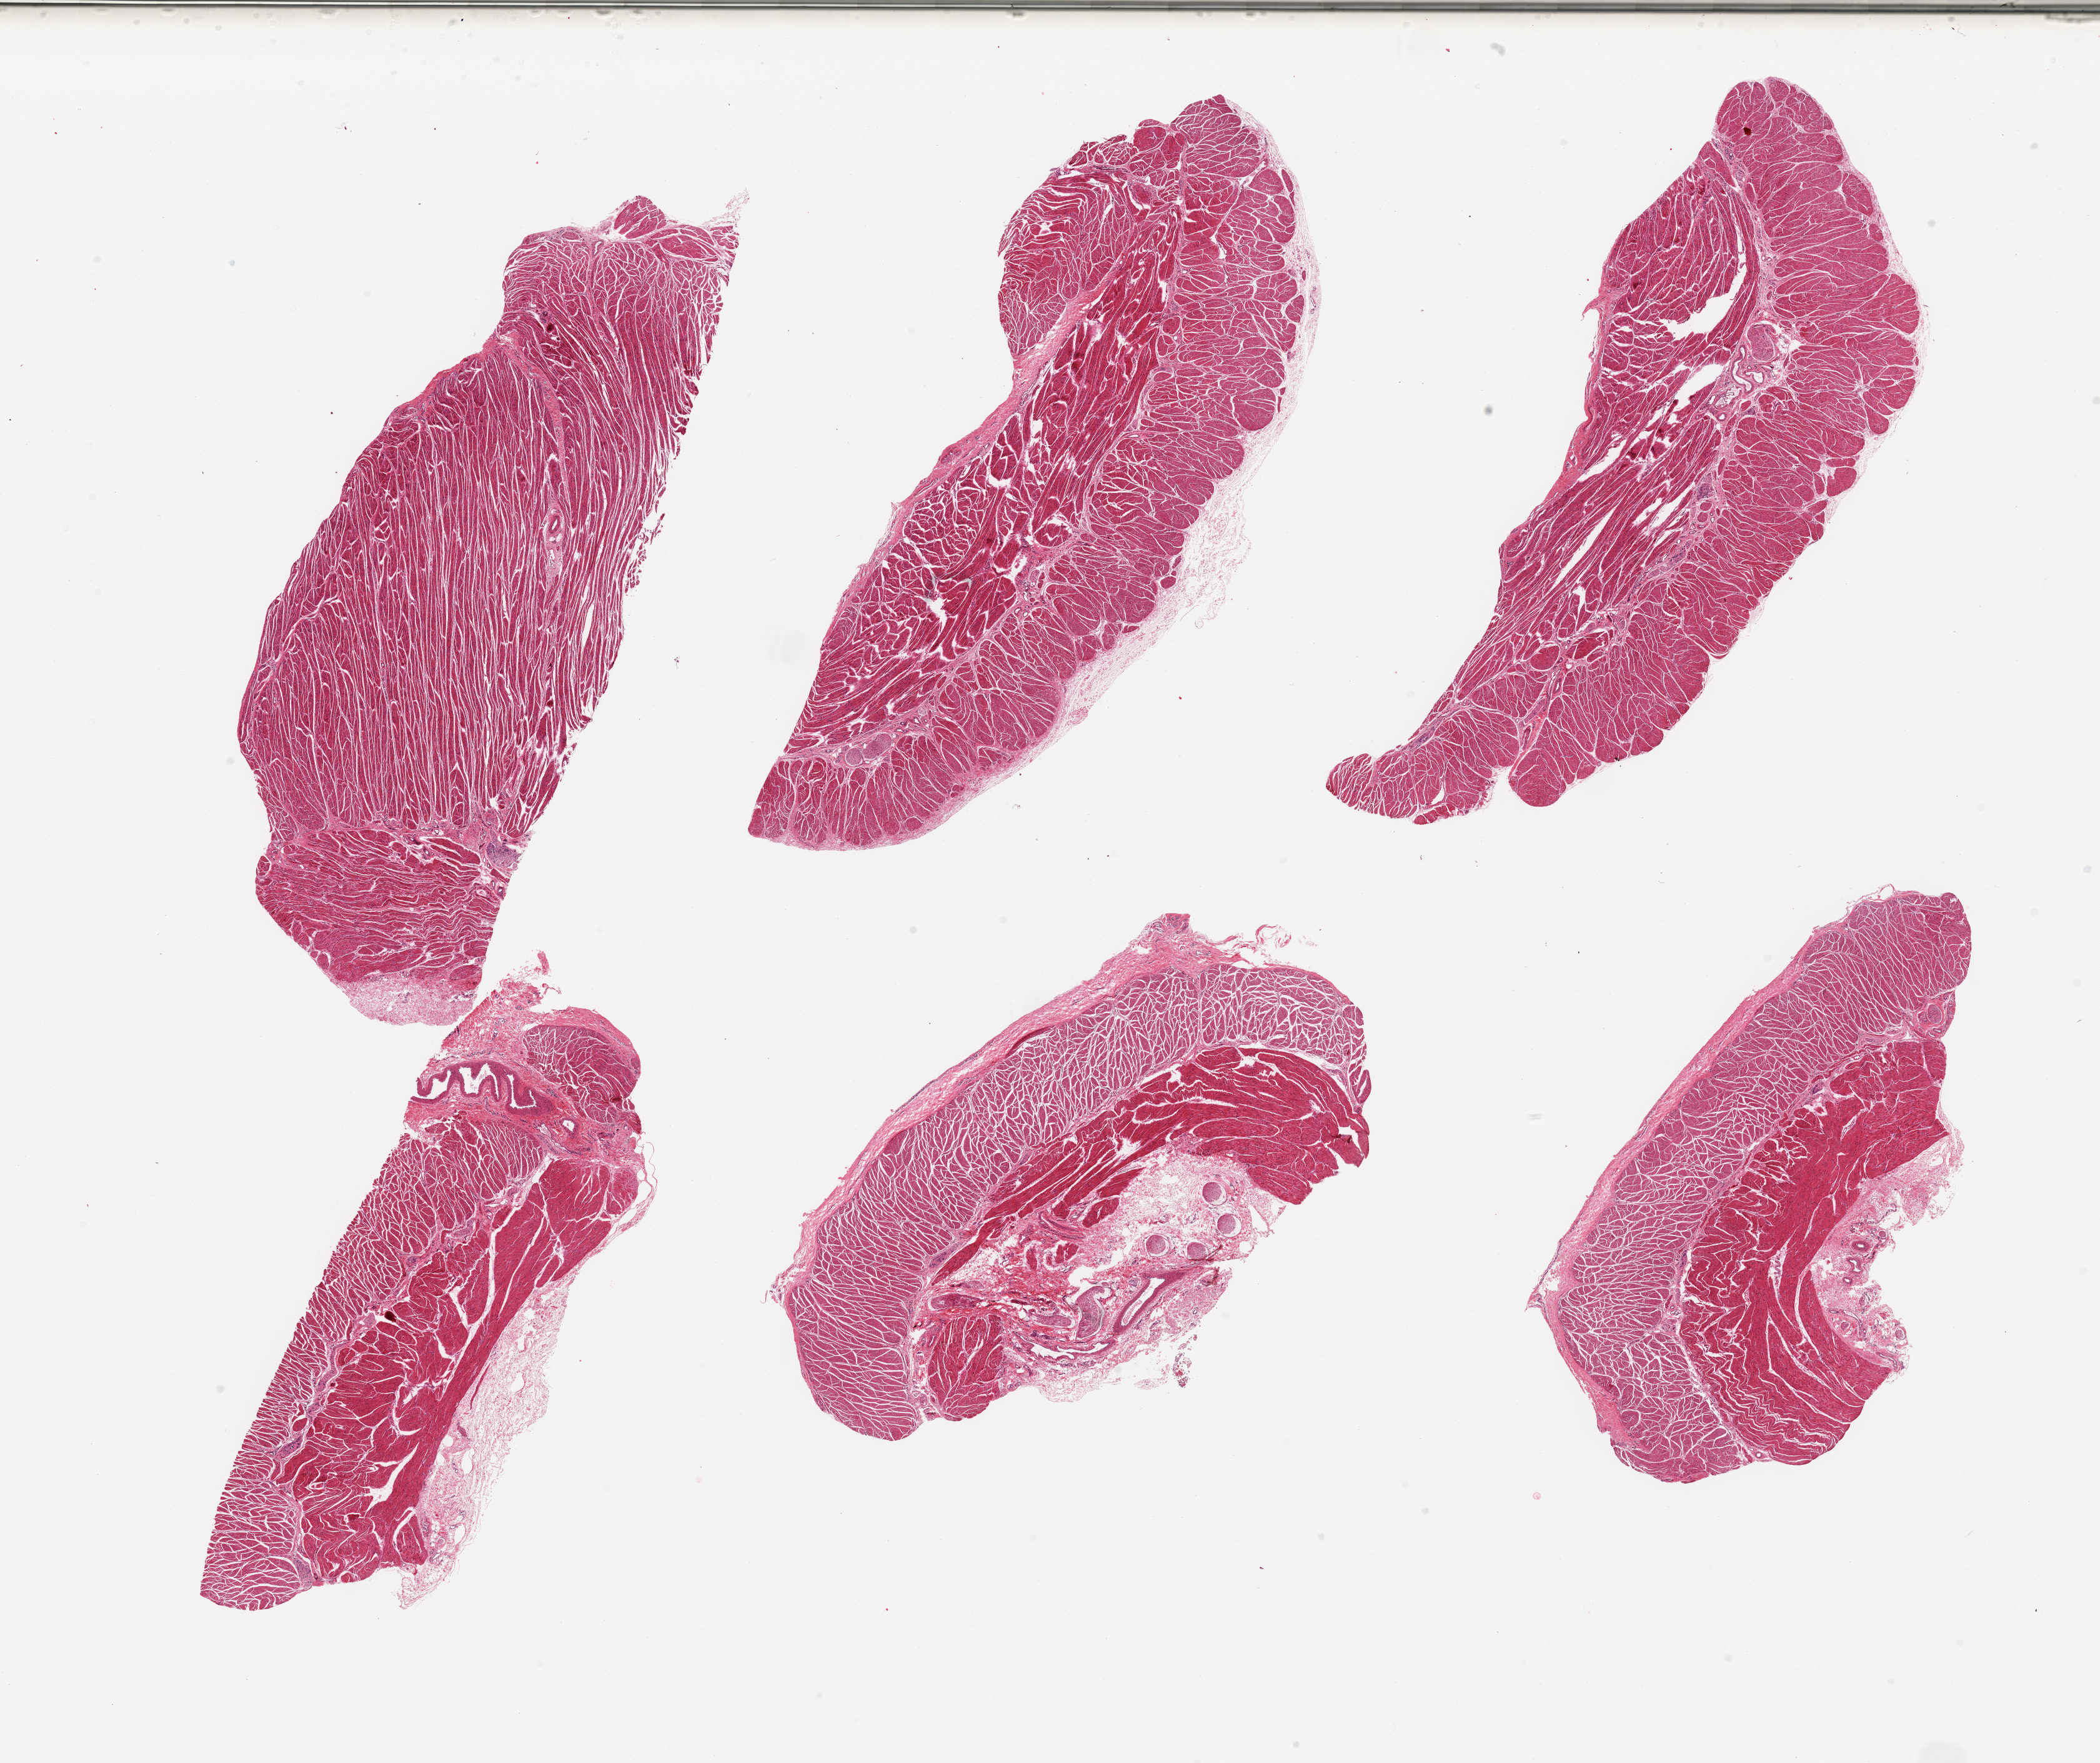
H&E whole-slide image, brightfield, a low-resolution overview of the entire scanned area, about 26.6 x 22.3 mm (acquisition: 20x scan), PAXgene-fixed, paraffin-embedded tissue, target tissue: gastroesophageal junction, tissue donor sample. Donor sex: female.
Pathologist's review note for this sample: 6 pieces, confirmed target muscularis.